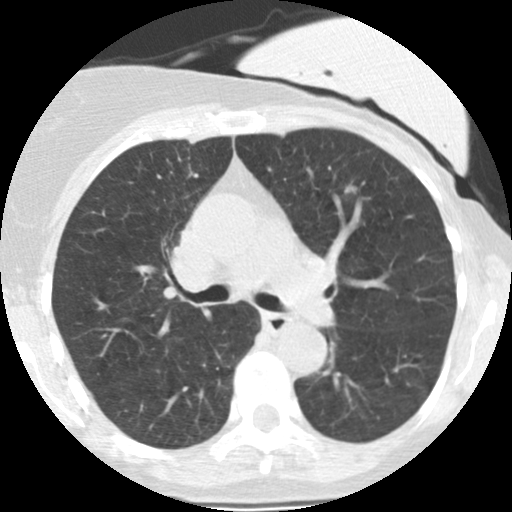
Low-dose screening chest CT, one axial slice; 120 kVp; lung window (W 1500 / L -600 HU); 512 × 512 image matrix, field of view 280 × 280 mm.
Outlined on this slice (manually delineated by an expert):
- lesion 1 (tumor, lower lobe of left lung): bounding box <345,185,356,193> (left, top, right, bottom; pixels)